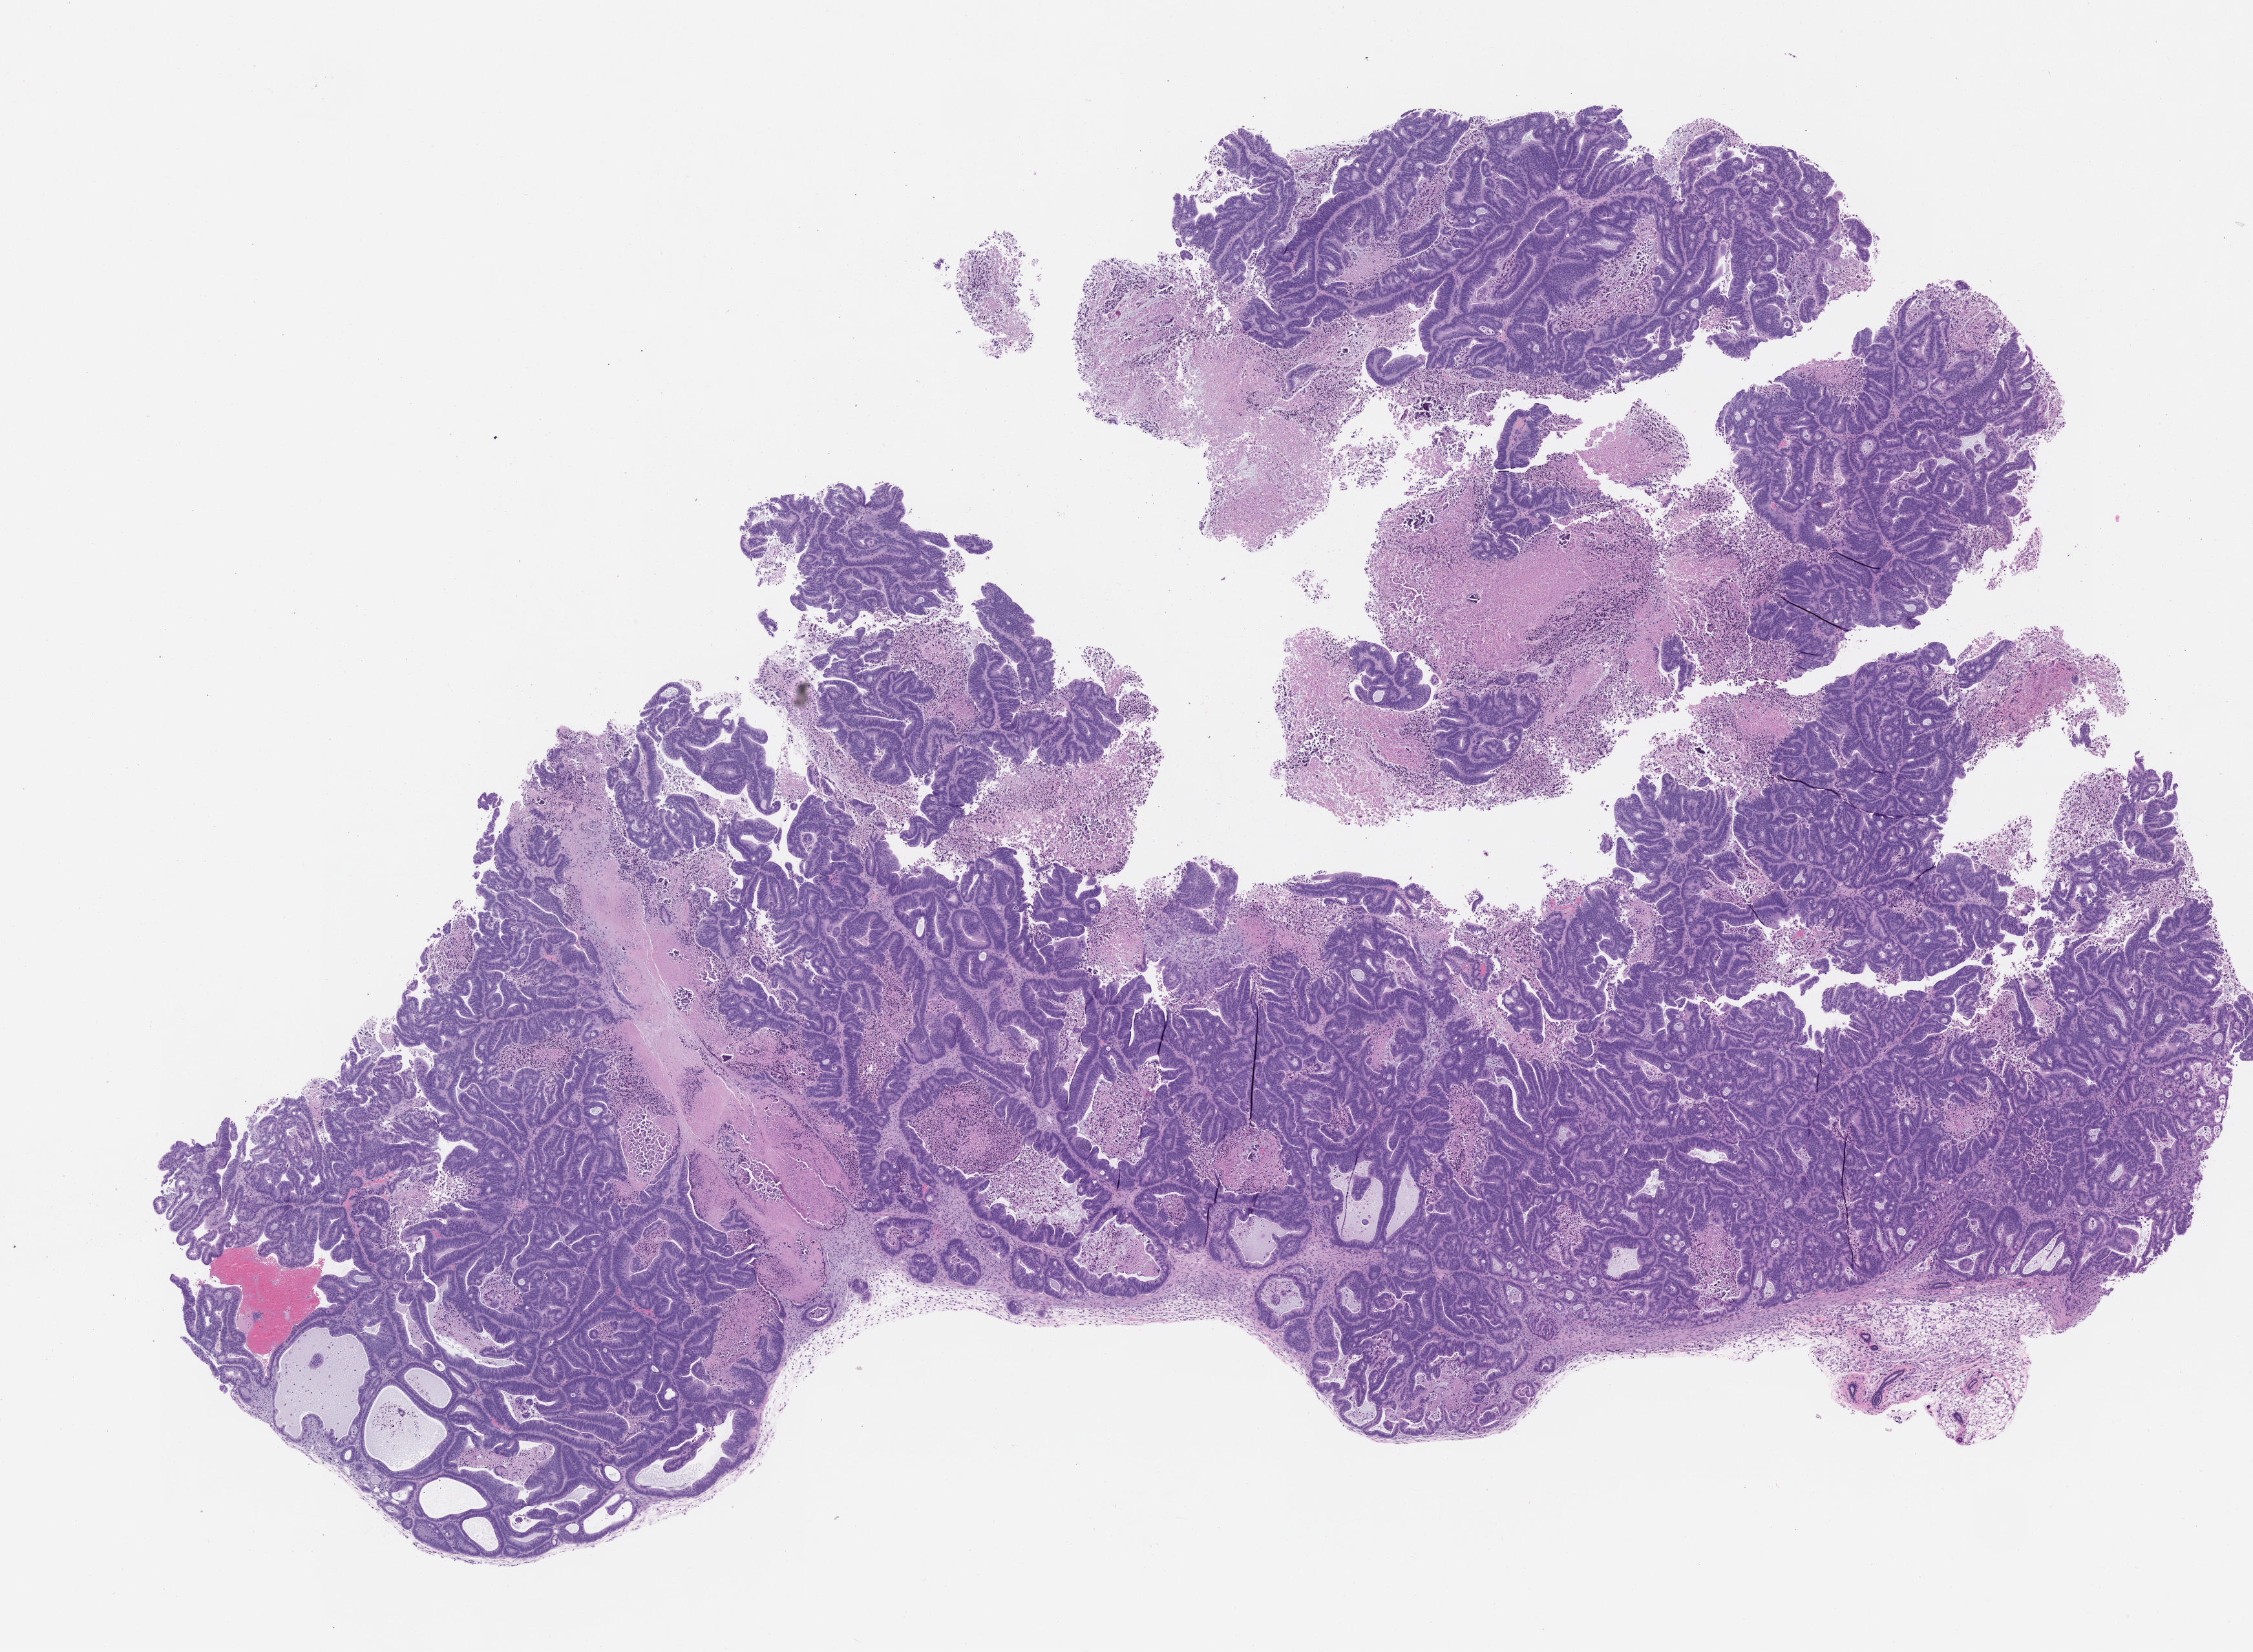
Whole-slide image, hematoxylin and eosin (H&E): patient-derived xenograft (human tumor grown in a mouse), passage 2 — shown as a low-resolution overview of the whole scanned area (about 14.0 x 10.3 mm); formalin-fixed, paraffin-embedded (FFPE) tissue; tumor site category: colon.
- originating patient diagnosis: Colon Adenocarcinoma